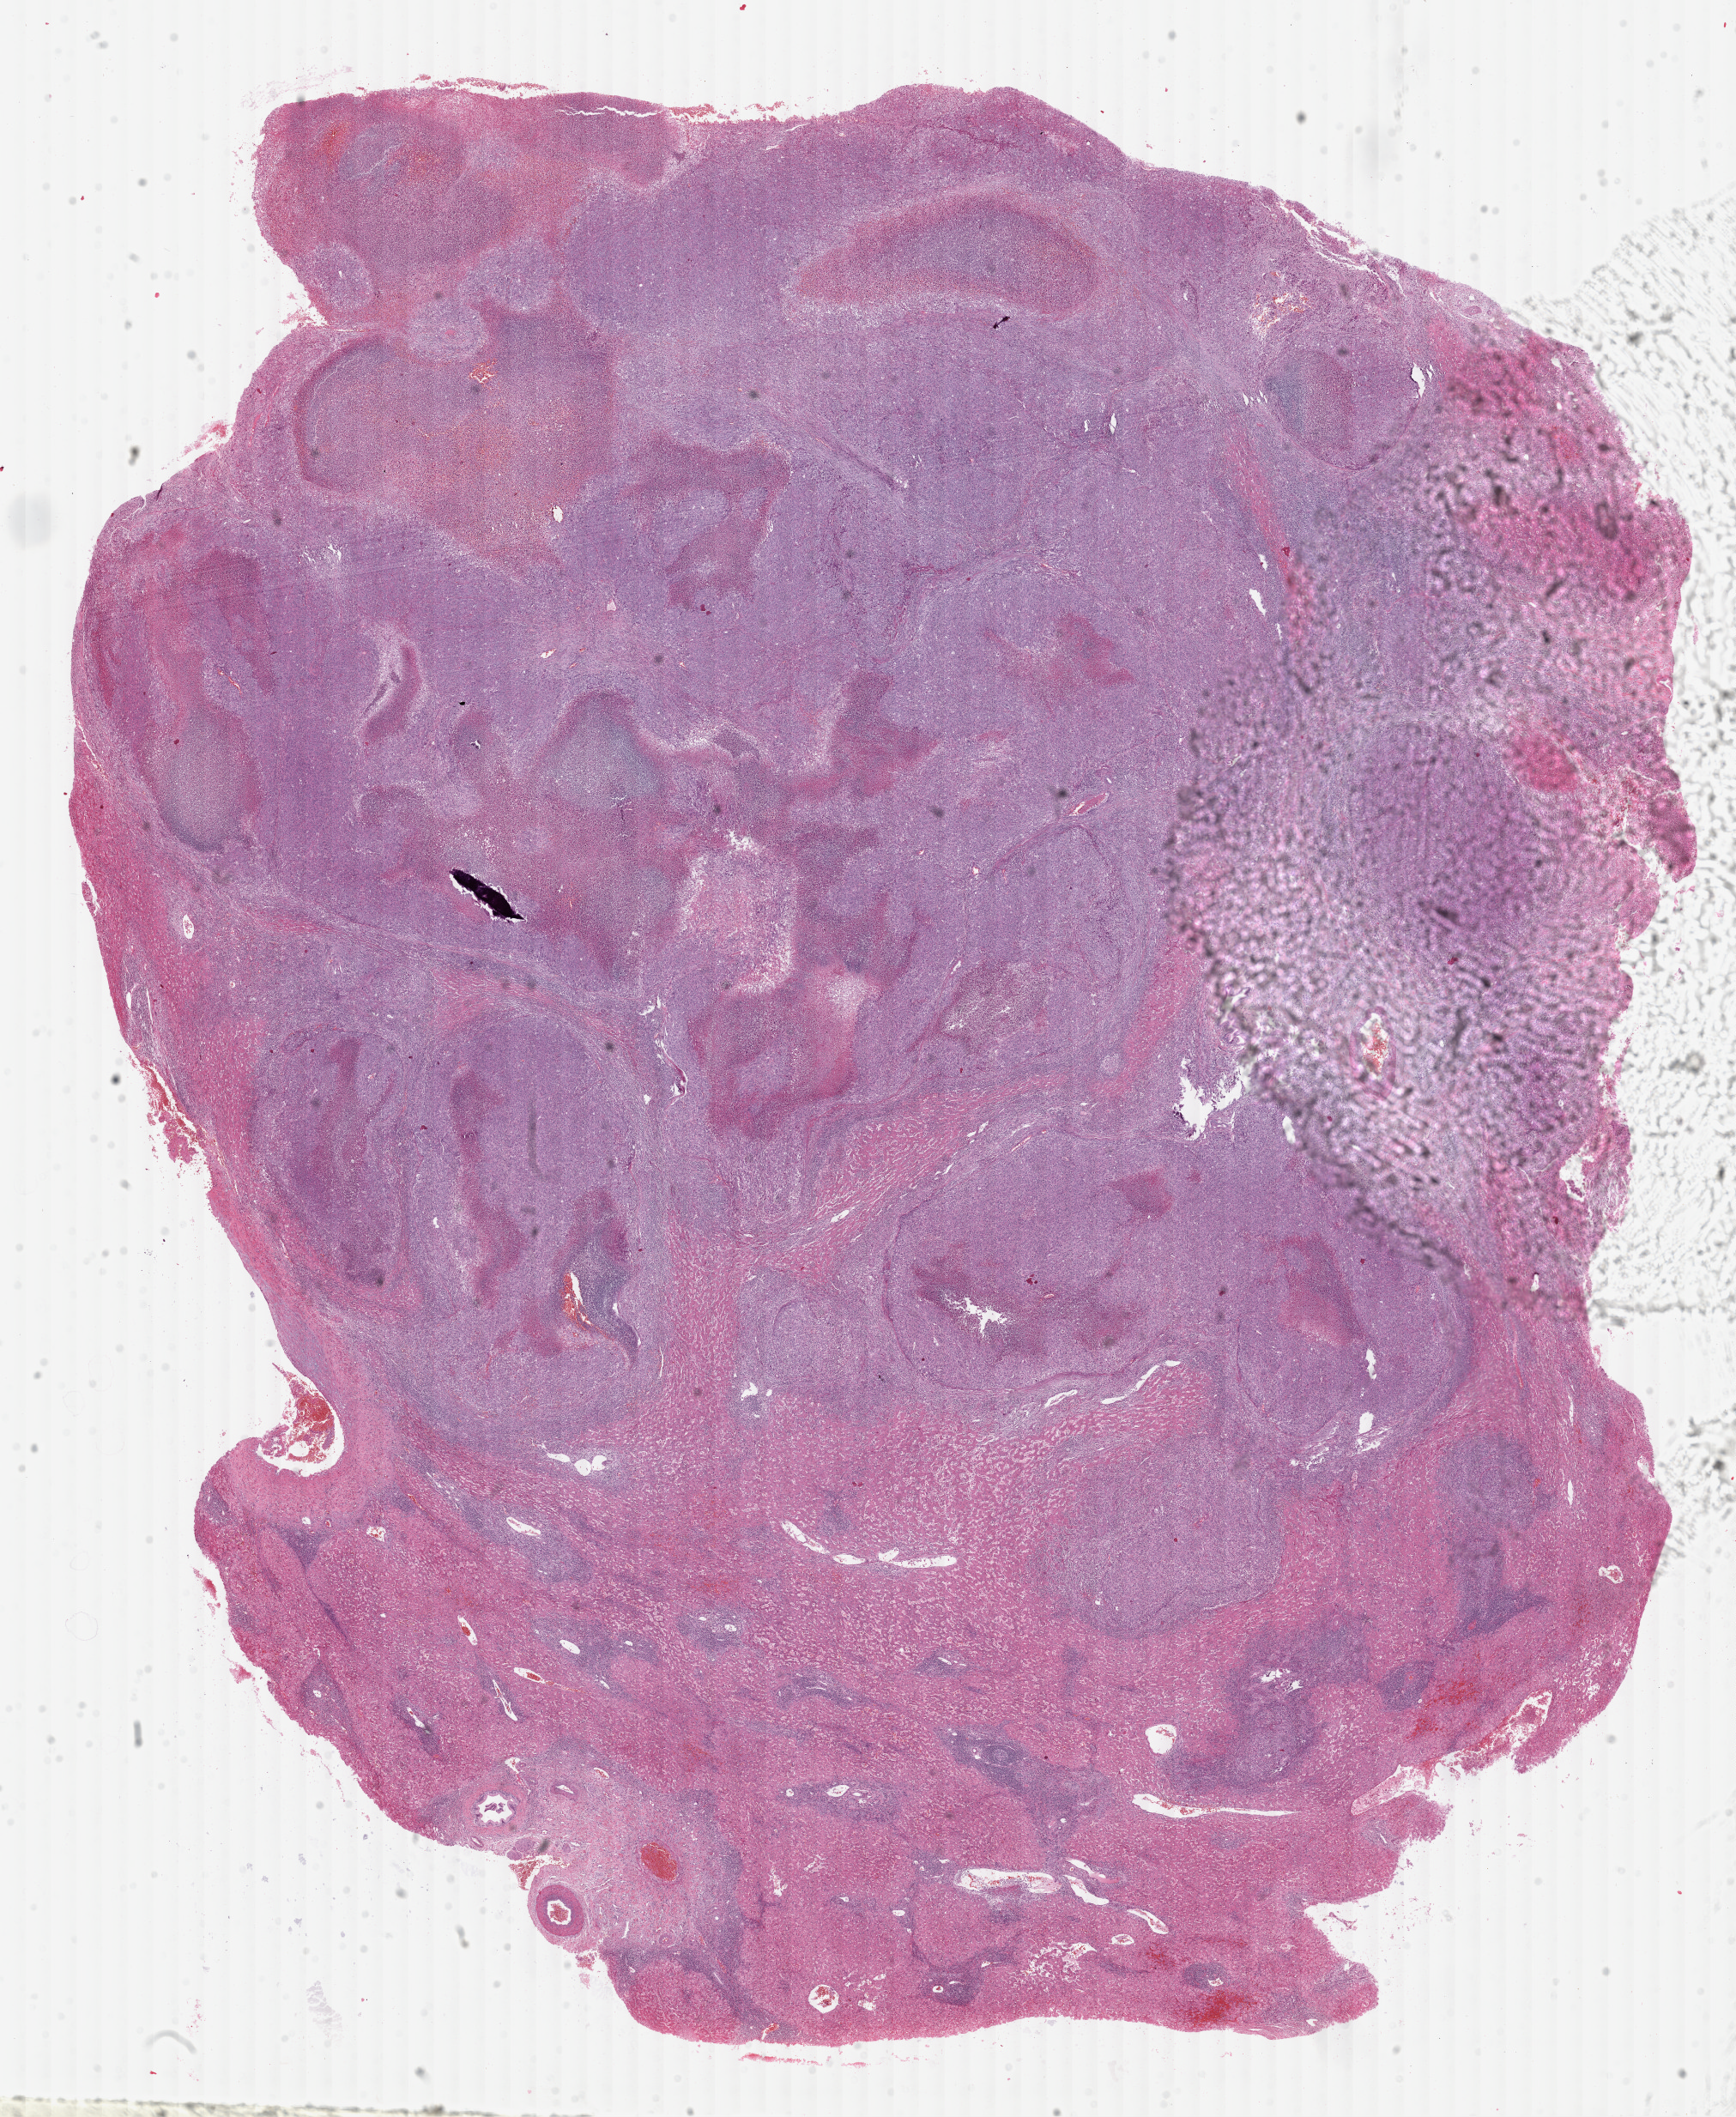
Whole-slide histology image, H&E — shown as a low-resolution overview of the whole scanned area (about 16.0 x 19.5 mm, acquisition: 40x scan). Formalin-fixed paraffin-embedded (FFPE) diagnostic section. Liver, primary tumour sample. Patient: male, age at initial diagnosis 50 years. Histologic grade: G3 (poorly differentiated).
• histologic diagnosis: Hepatocellular carcinoma, NOS
• AJCC pathologic stage: IIIA (6th edition)
• TNM: T3 N0 M0